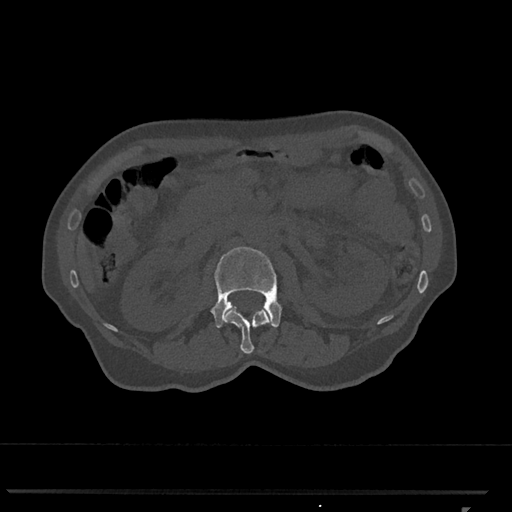
CT including the spine, one axial slice. Slice 365 of 793 in the series (ordered by position). Reconstruction kernel Br40s/3. 120 kVp. Bone window (W 1800 / L 400 HU). 0.5 mm slice thickness. 512 × 512 image matrix, field of view 380 × 380 mm. Female patient, age 62 years. Case-level facts recorded for this patient, not image findings: primary cancer: renal.
Outlined on this slice (semi-automatic segmentation, software-assisted and operator-edited):
- L1 vertebra: bounding box (x1, y1, x2, y2) in pixels: (223, 308, 272, 354)
- L2 vertebra: (211, 247, 282, 328)